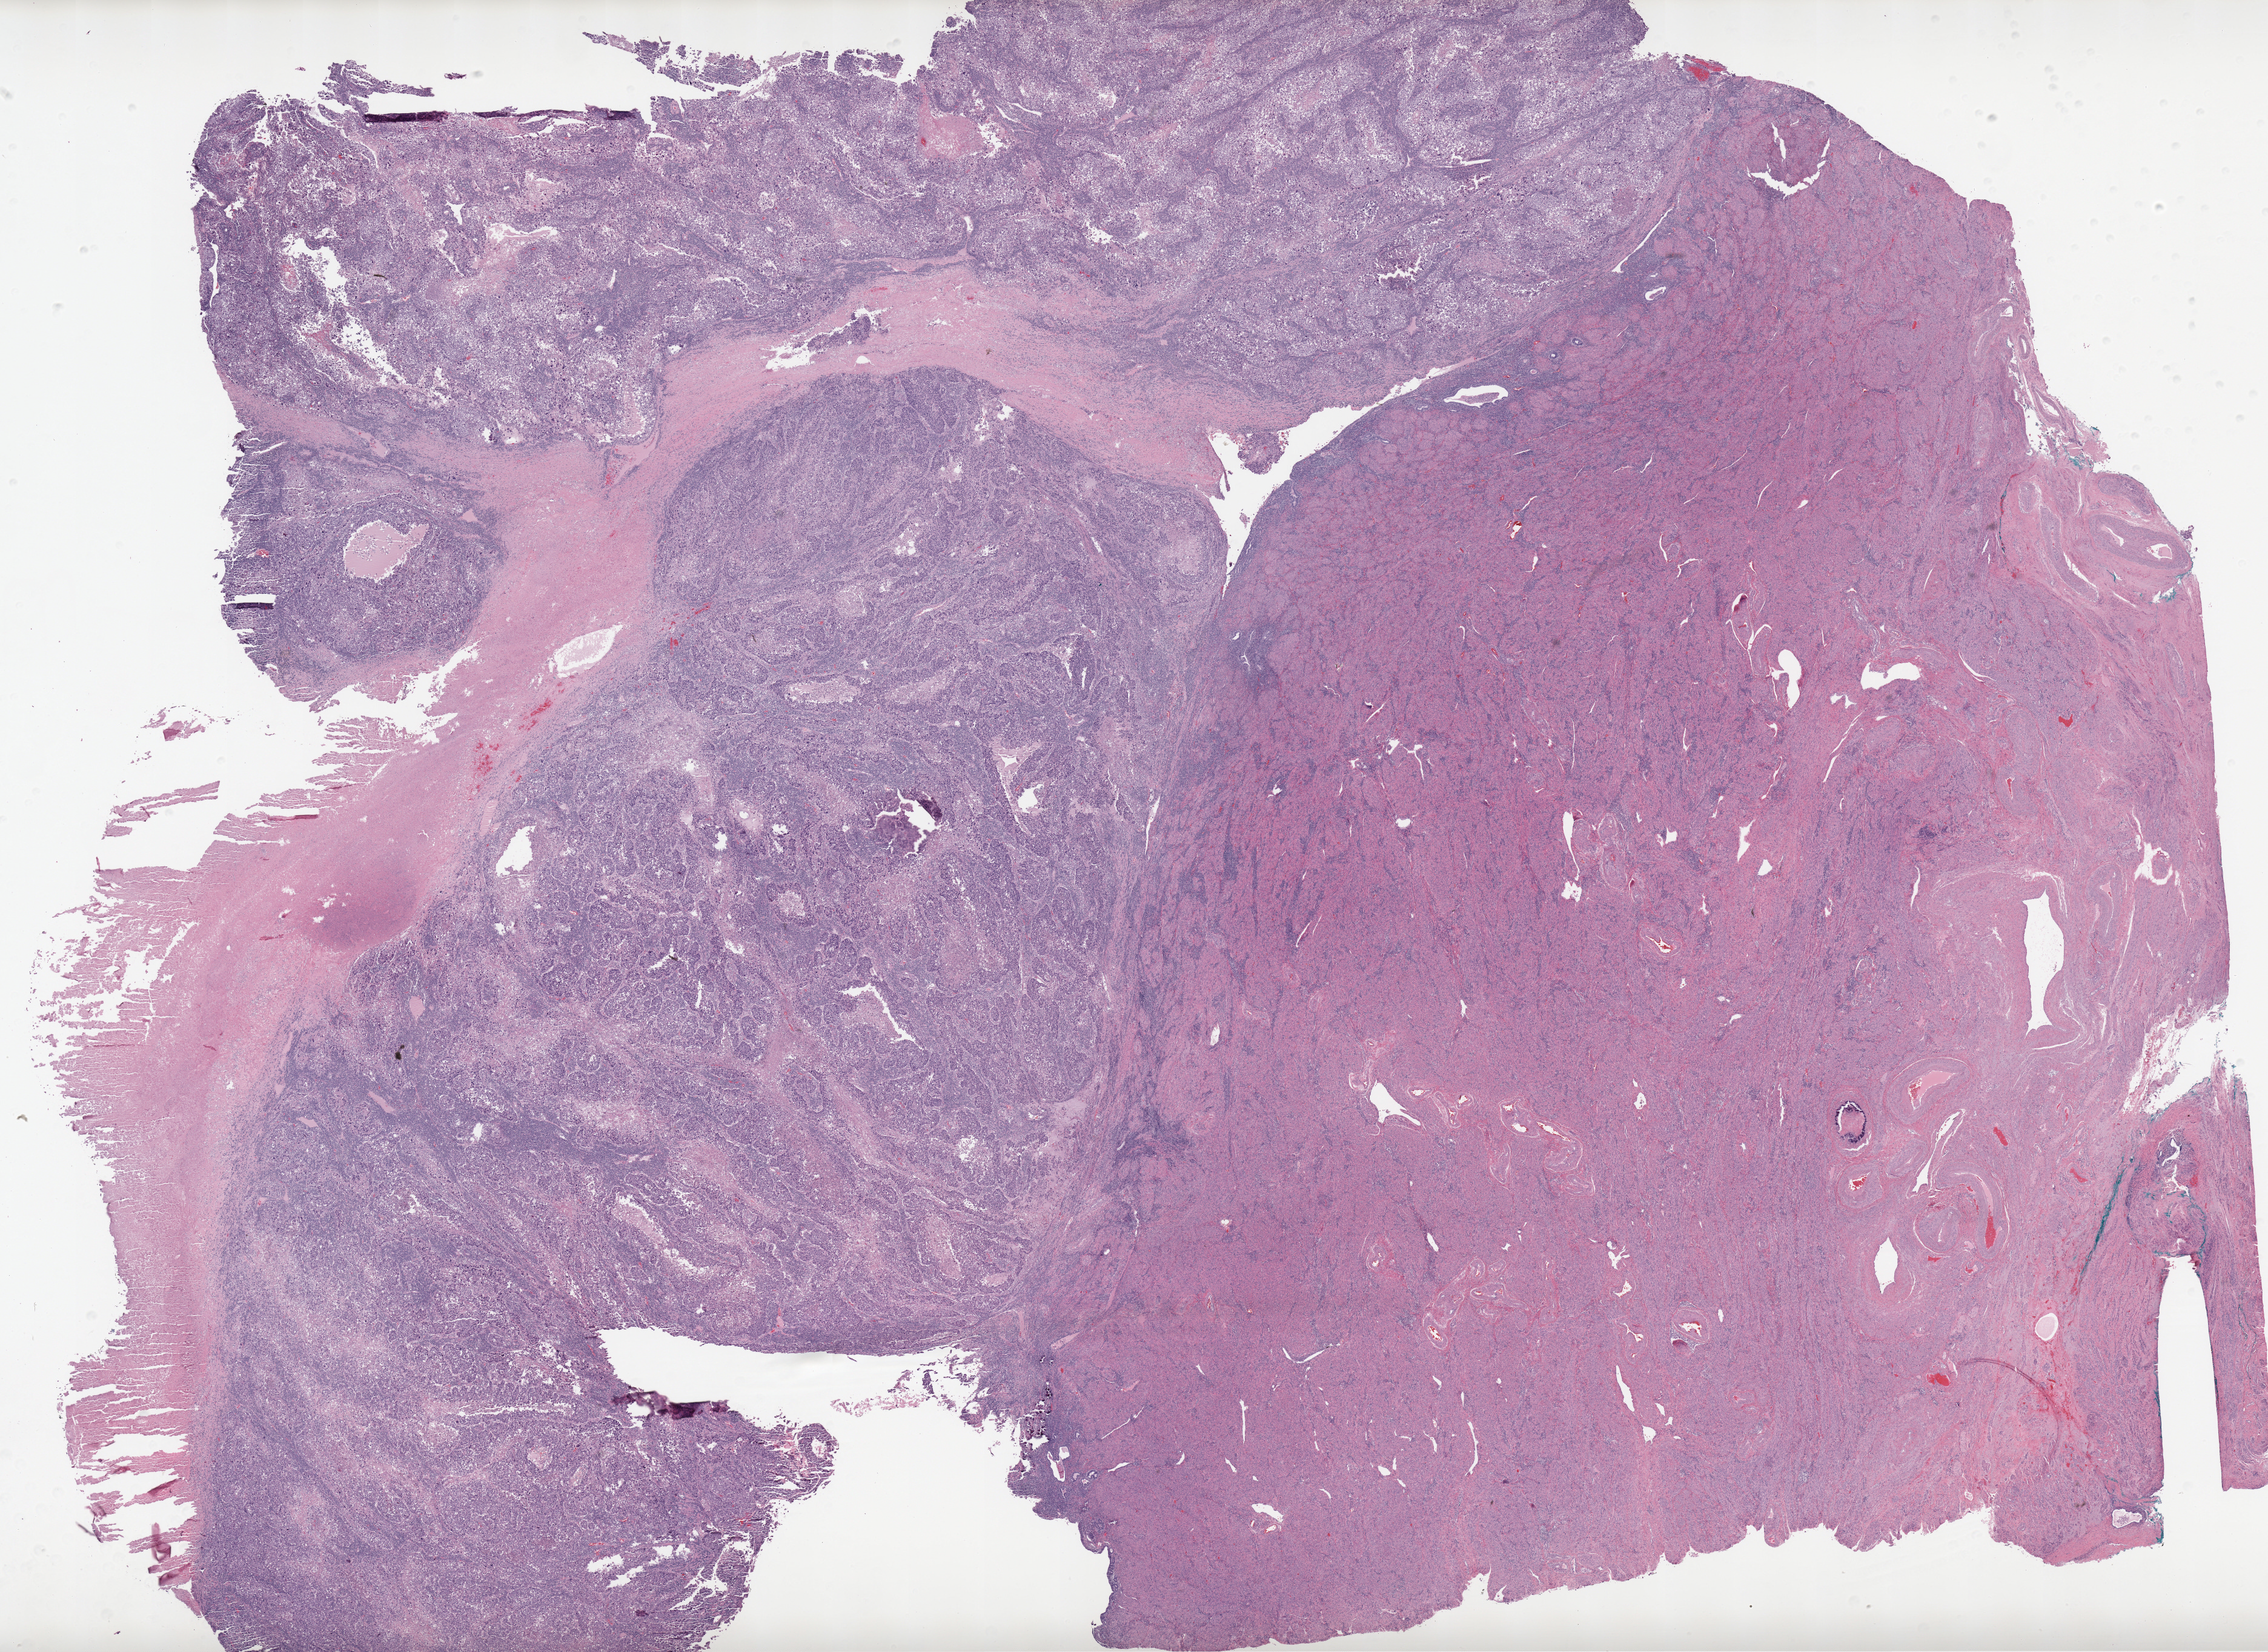
Whole-slide histology image, Hematoxylin and eosin (H&E) stained — low-resolution overview of the scanned area, about 29.8 x 21.7 mm (from a 20x scan), formalin-fixed paraffin-embedded (FFPE) diagnostic section, sample: primary tumour, uterus. Female patient. Histologic grade: G3 (poorly differentiated).
FIGO stage: IVB. Diagnosis: Endometrioid adenocarcinoma, NOS (endometrium).